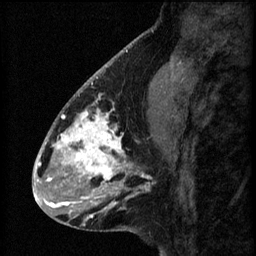
Breast MRI (dynamic contrast-enhanced), one sagittal slice; slice 23 of 60 in the series (ordered by position); 3 images stored at this slice position (order not interpretable as contrast timing); 1.5 T; TE 4.2 ms, TR 8.2 ms; 256 × 256 image matrix. Female patient, age 41 years.
Outlined on this slice (semi-automatic segmentation, software-assisted and operator-edited):
- analysis volume of interest (the breast-tissue region the enhancement analysis was run in; not a lesion): bounding box [x1, y1, x2, y2] px = [56, 104, 157, 207]
- tumour enhancement mask (voxels above the 70 % enhancement threshold inside the analysis volume of interest): [56, 104, 150, 207]